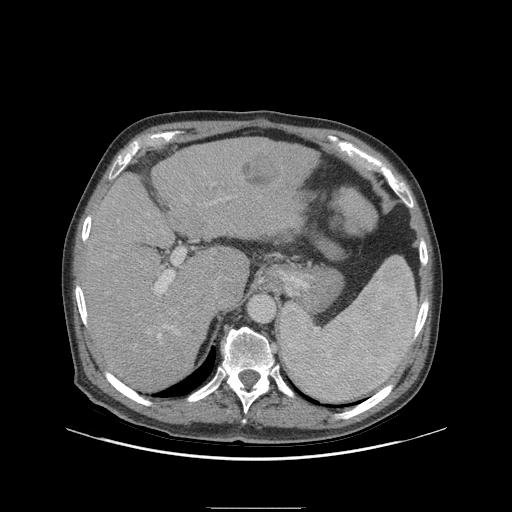
Contrast-enhanced abdominal CT (liver protocol), one axial slice; position 66 of 105 along the scan axis; reconstruction kernel STANDARD; 140 kVp; soft-tissue window (W 400 / L 40 HU); 2.5 mm slice thickness; 512 × 512 image matrix, field of view 440 × 440 mm. From the clinical record (not read from this slice): diagnosis: hepatocellular carcinoma (patient treated with transarterial chemoembolisation; whether this scan precedes or follows treatment is not stated here); TNM stage (as recorded): Stage-I; Child-Pugh class: A; tumour nodularity: uninodular; tumour size: 5.1 cm.
Outlined on this slice (semi-automatic segmentation, software-assisted and operator-edited):
- liver parenchyma outside the tumour (the mass and vessels are separate outlines, so this box may not span the whole liver): bounding box (x1, y1, x2, y2) in pixels: (80, 136, 364, 392)
- mass: (243, 151, 279, 187)
- liver vessels: (154, 197, 229, 338)